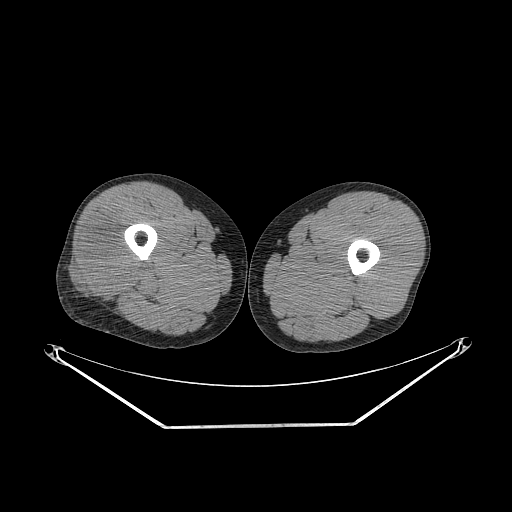
CT of an extremity soft-tissue mass (from a PET/CT study), one axial slice. Position 240 of 267 along the scan axis. Soft-tissue window (W 400 / L 40 HU). 512 × 512 image matrix, field of view 500 × 500 mm. Male patient. Case-level facts recorded for this patient, not image findings: histological type: poorly differentiated synovial sarcoma; grade: high; site of the primary tumour: right buttock.
Annotated regions visible in this slice (expert contour drawn on MRI and transferred to this co-registered scan by the dataset authors):
- gross tumour volume including surrounding oedema: bounding box <73,224,136,293> (left, top, right, bottom; pixels)
- gross tumour volume (mass): <80,226,136,293>